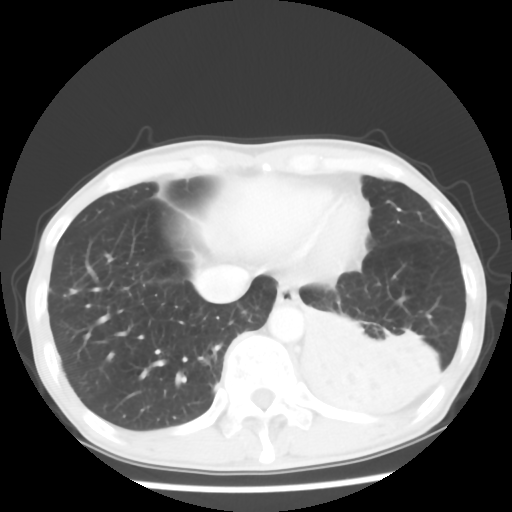
Chest CT, one axial slice. Slice 13 of 64 in the series (ordered by position). 120 kVp. Lung window (W 1500 / L -600 HU). 5 mm slice thickness. 512 × 512 image matrix, field of view 313 × 313 mm. Male patient, age 68 years. Case-level facts recorded for this patient, not image findings: clinical TNM (as recorded): T4 N0 M0.
Structures marked on this image (rectangle marked by the reading radiologist):
- lung tumour (recorded histology: squamous cell carcinoma): bounding box [x1, y1, x2, y2] px = [292, 295, 435, 431]